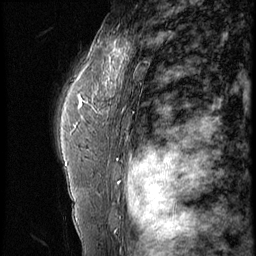
Breast MRI (dynamic contrast-enhanced), one sagittal slice. 4 images stored at this slice position (order not interpretable as contrast timing). 1.5 T. TE 4.2 ms, TR 9 ms. 2.5 mm slice thickness. 256 × 256 image matrix, field of view 180 × 180 mm. Patient: female, 44 years. From the clinical record (not read from this slice): setting: breast cancer imaged before/during neoadjuvant chemotherapy; receptor status: triple-negative.
Outlined on this slice (semi-automatically segmented with operator editing):
- analysis volume of interest (the breast-tissue region the enhancement analysis was run in; not a lesion): bounding box (x1, y1, x2, y2) in pixels: (87, 28, 132, 99)
- tumour enhancement mask (voxels above the 140 % enhancement threshold inside the analysis volume of interest): (105, 42, 129, 84)